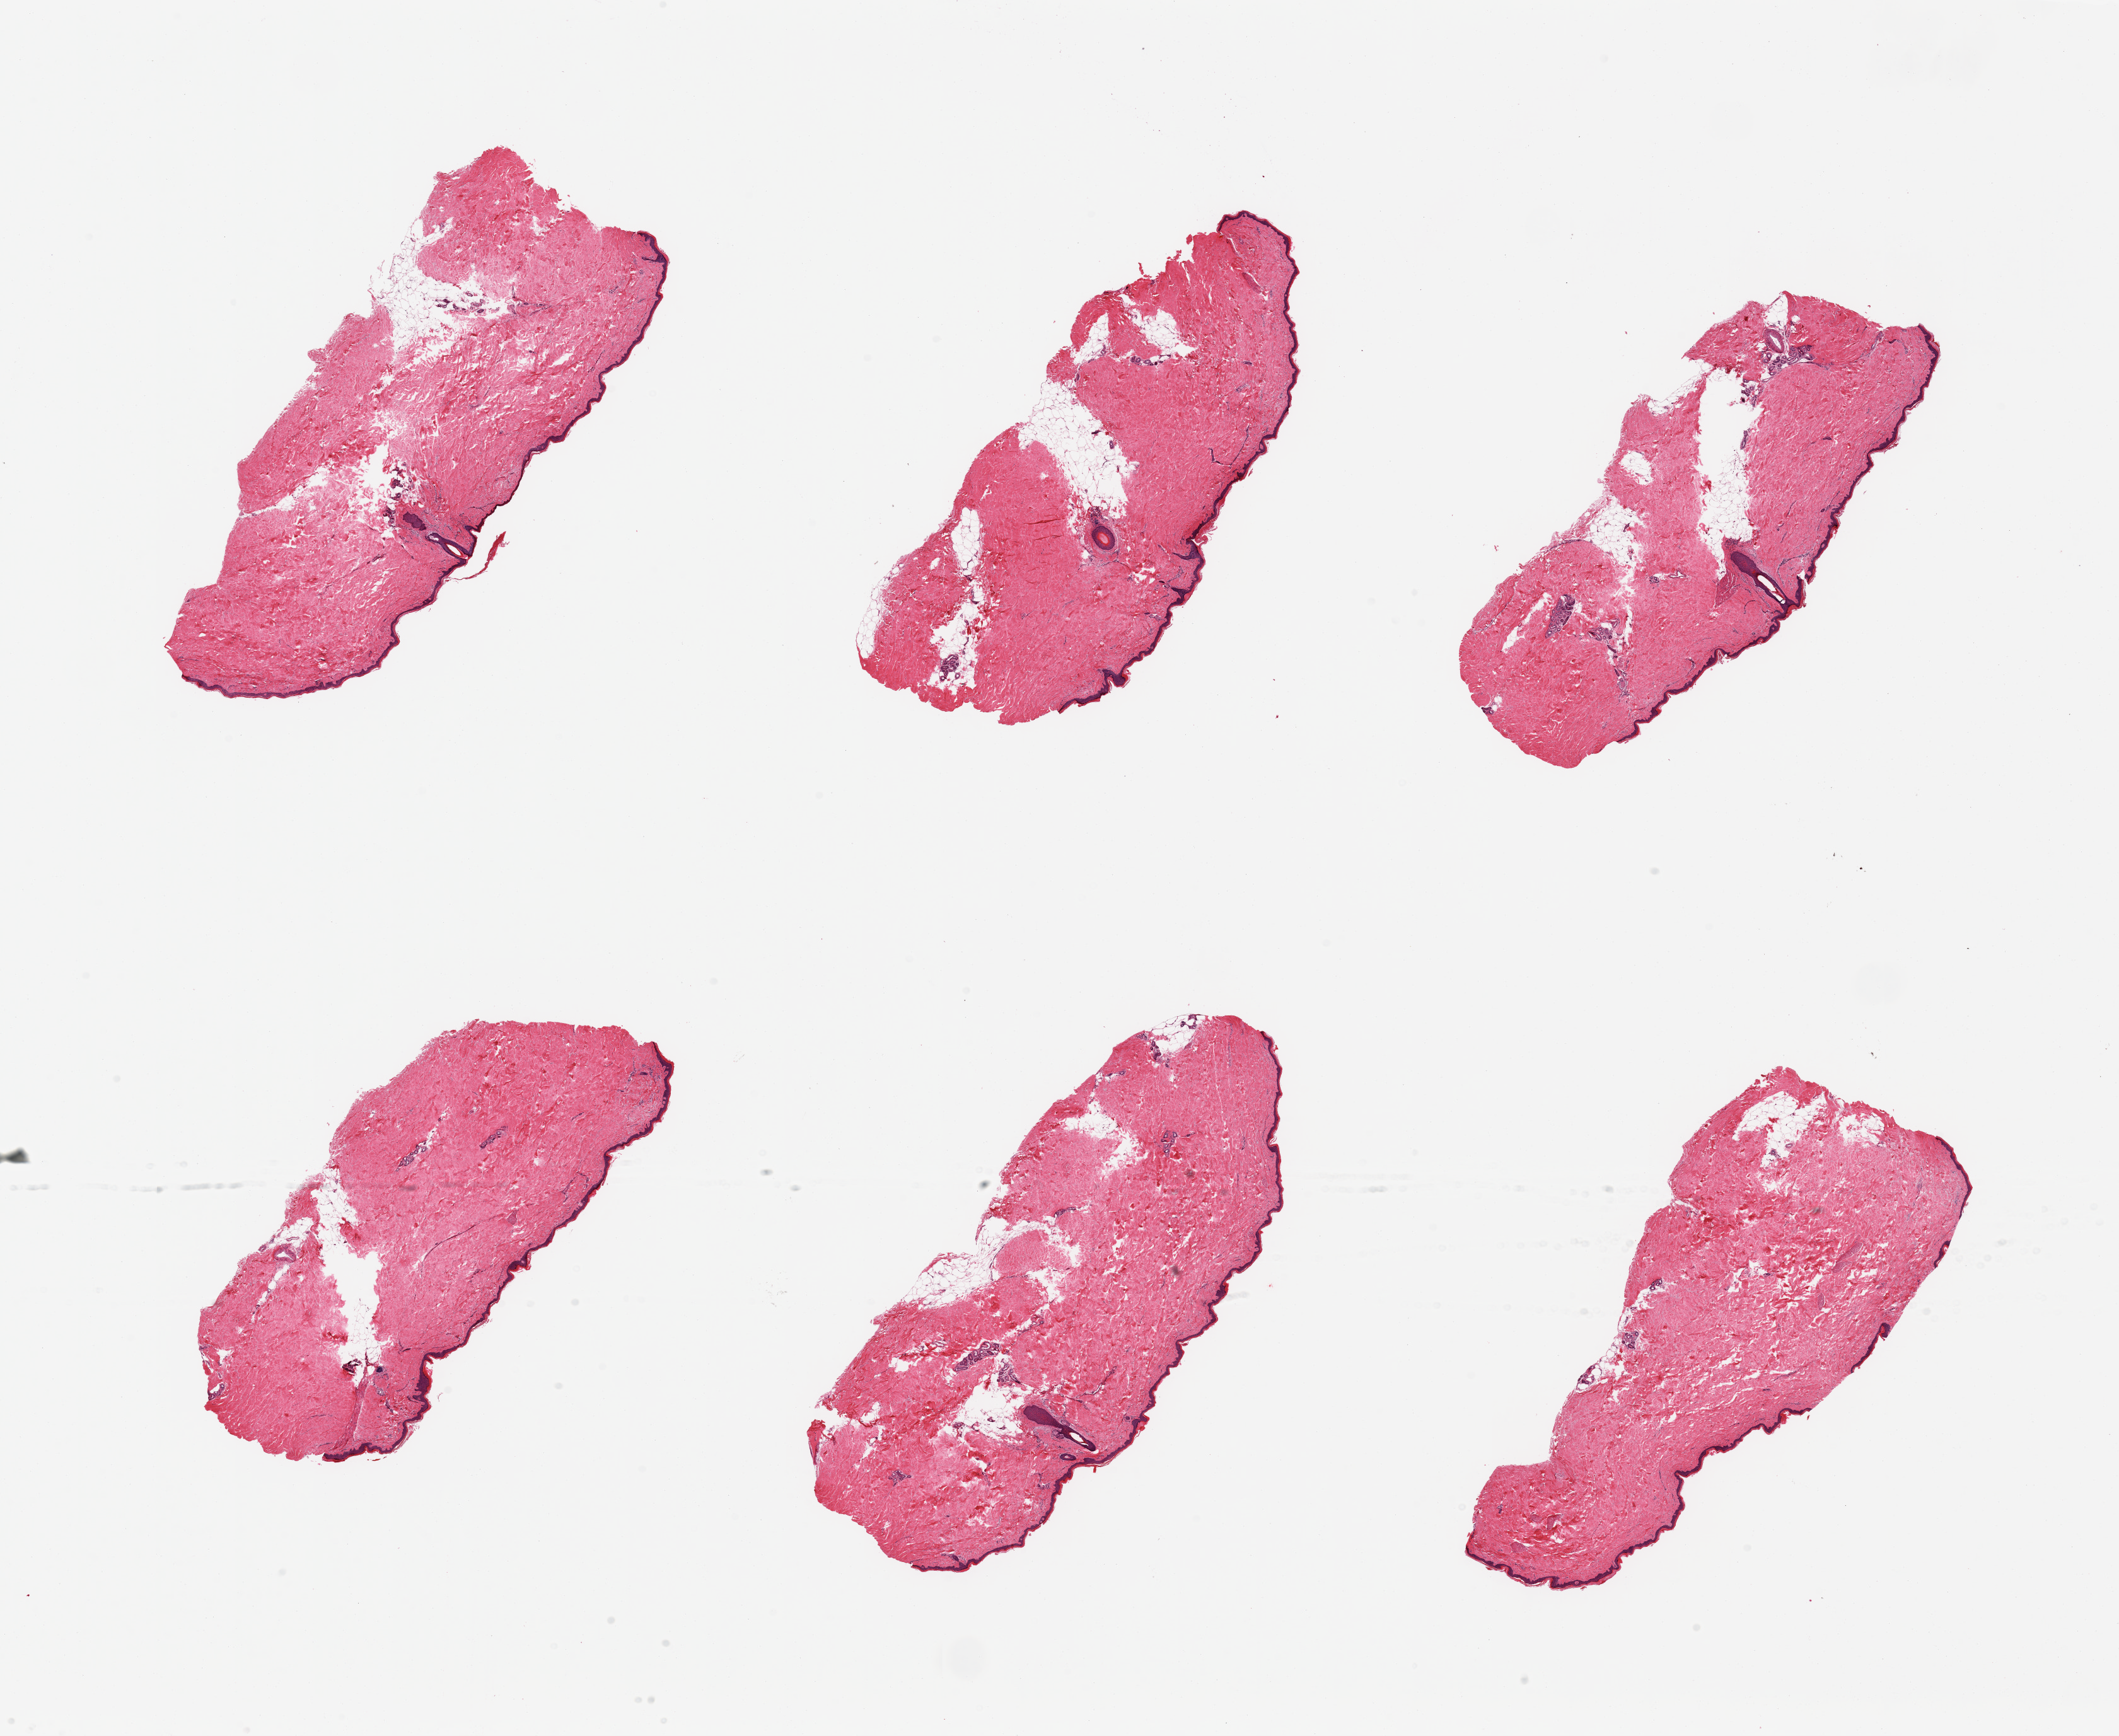
Hematoxylin and eosin (H&E) whole-slide image, low-resolution overview of the scanned area, about 26.6 x 21.8 mm (slide scanned at 20x), PAXgene-fixed, paraffin-embedded tissue, section of skin of lower leg (target tissue), donor tissue sample. Donor sex: male.
Reviewer comment on this tissue sample: 6 pieces; well trimmed; up to 10% dermal fat.